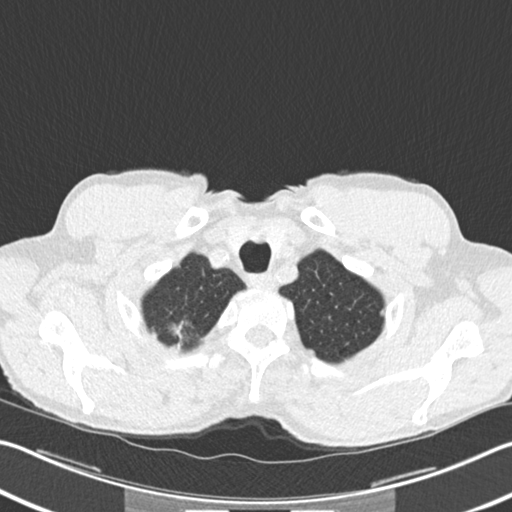
Chest CT (low-dose screening protocol), one axial image; second annual screen; lung window (W 1500 / L -600 HU); 2 mm slice thickness; standard (soft-tissue) reconstruction kernel (B30f); 512 × 512 image matrix, field of view 342 × 342 mm. Male, age 62 years at enrolment.
Expert reader's lesion annotation, box from (x=157, y=310) to (x=203, y=352) px. The screening reader recorded 2 non-calcified nodules or masses ≥4 mm on this exam (right upper lobe, right upper lobe); which of them this box marks is not recorded. Official screen result: positive, change unspecified: nodule(s) >= 4 mm or enlarging nodule(s), mass(es), or other non-specific abnormalities suspicious for lung cancer. Lung cancer was diagnosed 5 days after this screen: bronchiolo-alveolar adenocarcinoma, NOS, right upper lobe, well differentiated (G1), stage IA (AJCC 6th edition), 15 mm at pathology.